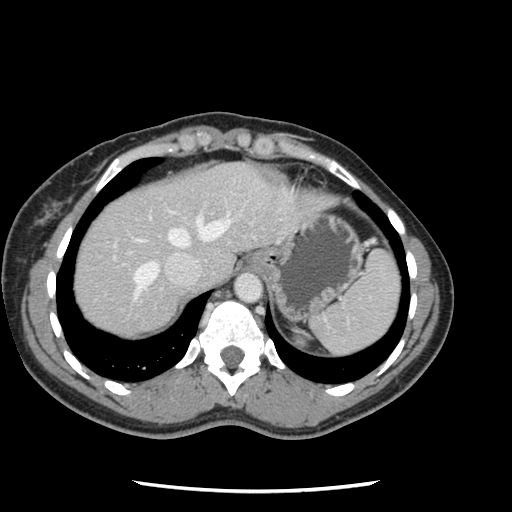
Contrast-enhanced abdominal CT, one axial slice. Position 102 of 134 along the scan axis. Intravenous contrast given. Soft-tissue window (W 400 / L 40 HU). 2.5 mm slice thickness. 512 × 512 image matrix, field of view 330 × 330 mm. Female patient, age 43 years. From the clinical record (not read from this slice): diagnosis: colorectal cancer liver metastases, imaged before liver resection; multiple liver metastases: yes; largest metastasis: 3.4 cm.
Annotated regions visible in this slice (outlined manually by an expert reader):
- hepatic veins: box from (x=133, y=215) to (x=231, y=299) px
- liver: (x=73, y=162)–(x=319, y=335)
- planned liver remnant (the part of the liver to remain after resection): (x=73, y=177)–(x=198, y=306)
- portal vein (with intrahepatic branches): (x=113, y=241)–(x=132, y=260)